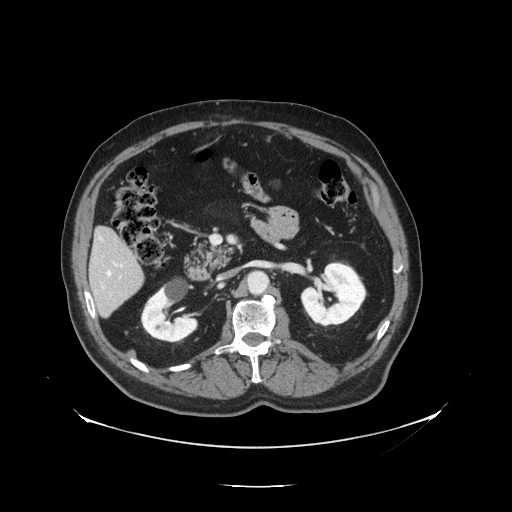
Contrast-enhanced abdominal CT, one axial slice; position 58 of 138 along the scan axis; reconstruction kernel STANDARD; 120 kVp; intravenous contrast given; soft-tissue window (W 400 / L 40 HU); 2.5 mm slice thickness; 512 × 512 image matrix. Male patient, age 77 years. Case-level facts recorded for this patient, not image findings: diagnosis: colorectal cancer liver metastases, imaged before liver resection; multiple liver metastases: no; largest metastasis: 1.5 cm.
Structures marked on this image (manually delineated by an expert):
- liver: bounding box (x1, y1, x2, y2) in pixels: (91, 229, 143, 316)
- planned liver remnant (the part of the liver to remain after resection): (92, 229, 140, 284)